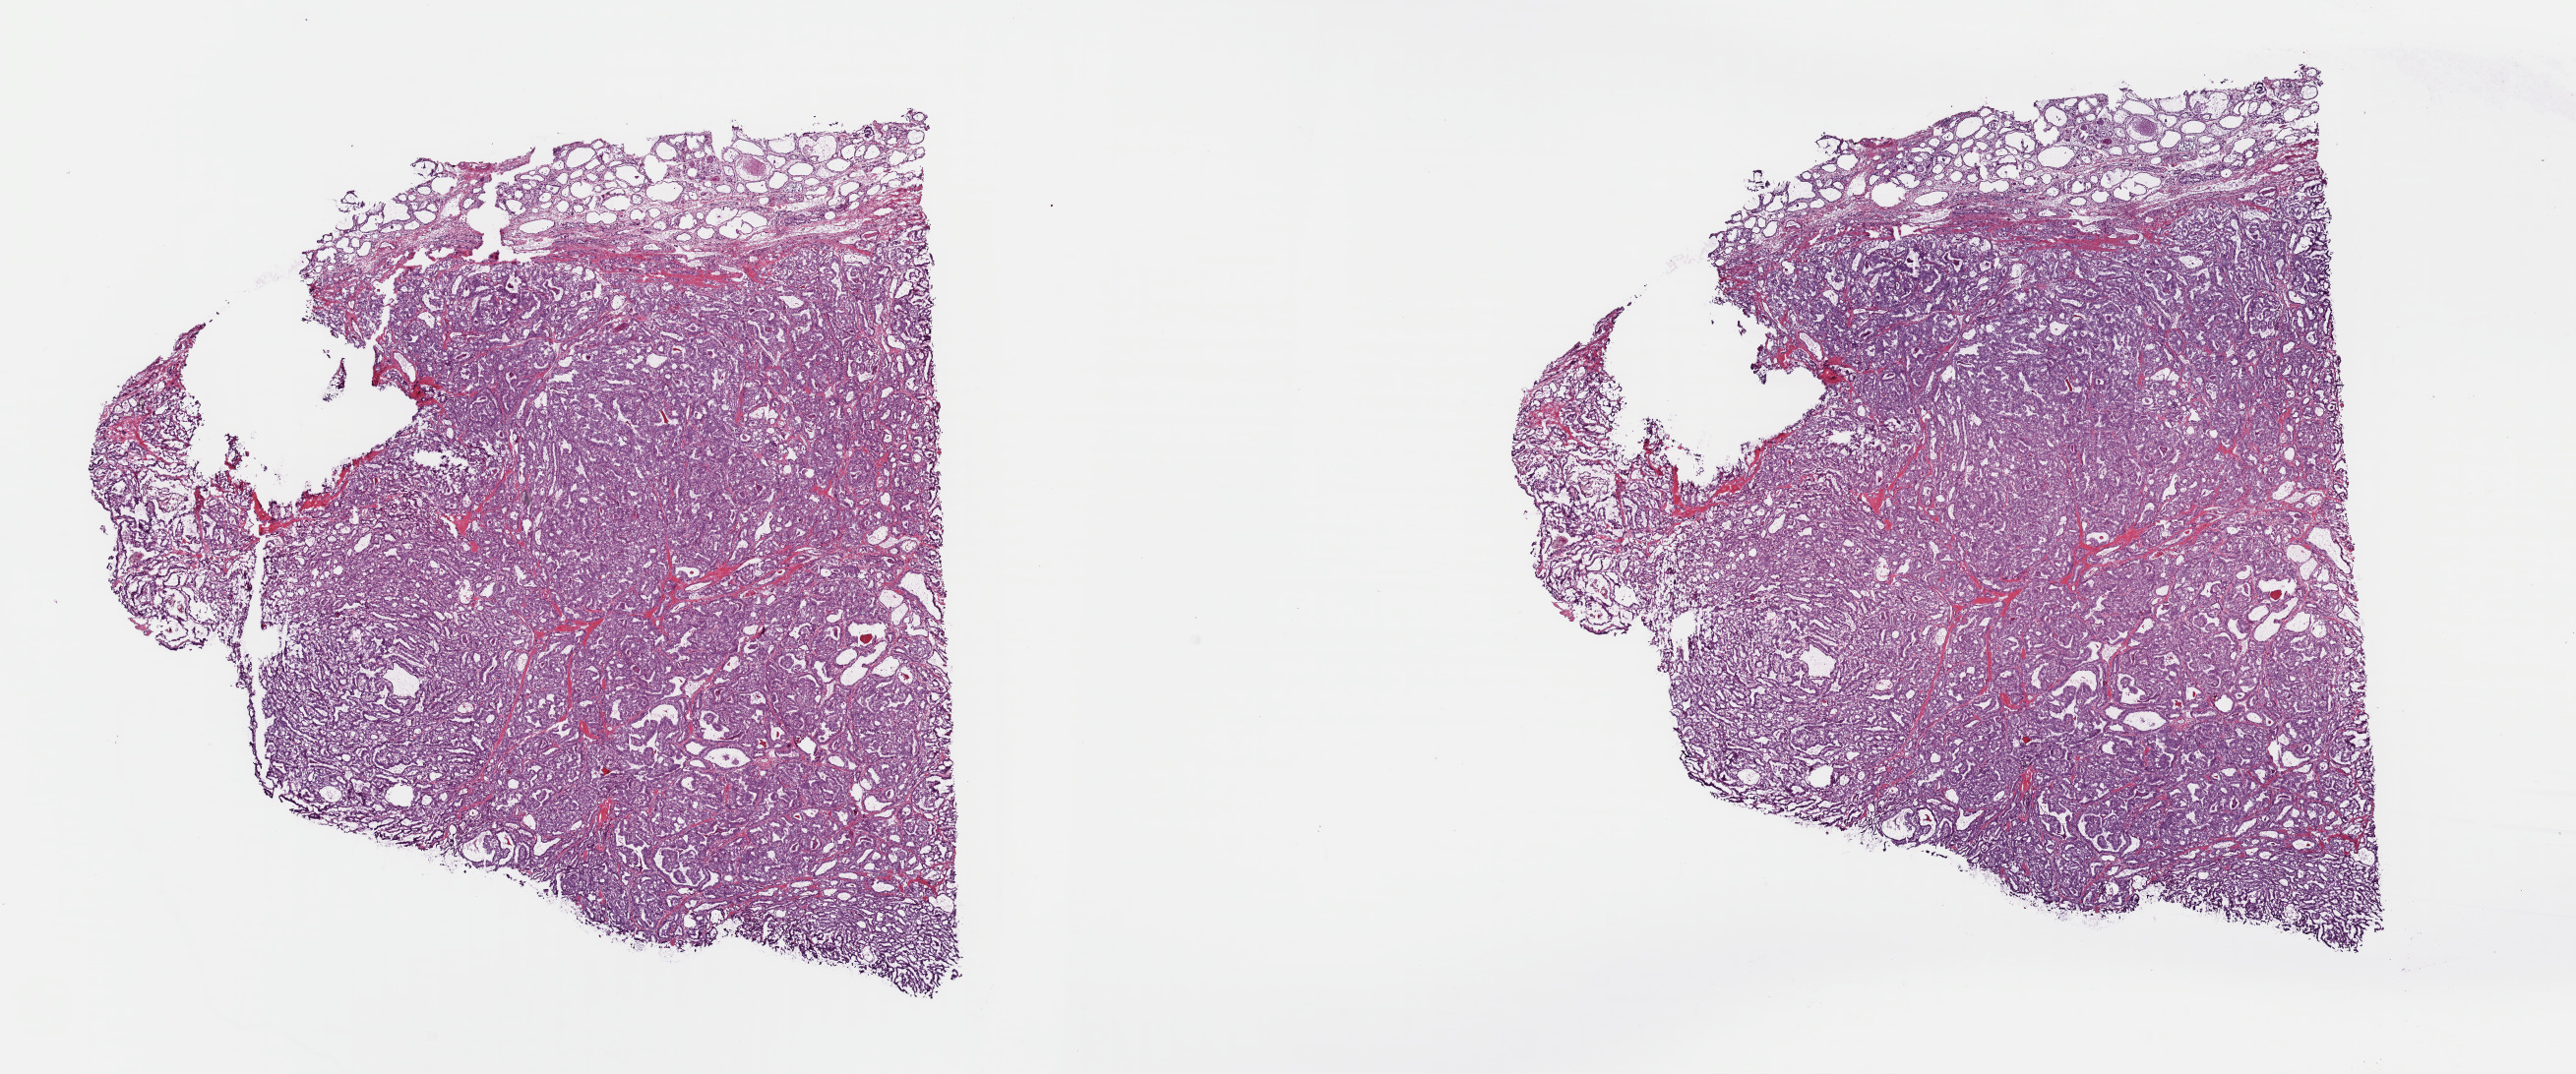
Whole-slide histology image, H&E-stained, whole scanned area (about 20.7 x 8.6 mm) shown as a low-resolution overview, frozen section, sample: primary tumour, thyroid. Female, age 51 years at initial diagnosis. Pathologist review of this section (percent, as recorded): tumour cells 95%, tumour nuclei 90%, normal cells 5%, stromal cells 0%, necrosis 0%. Inflammatory infiltration, as recorded: lymphocyte infiltration 0%, monocyte infiltration 0%, neutrophil infiltration 0%.
* TNM: T1b N0 M0
* histologic diagnosis: Papillary adenocarcinoma, NOS (thyroid gland)
* AJCC pathologic stage: I (7th edition)
* laterality: left